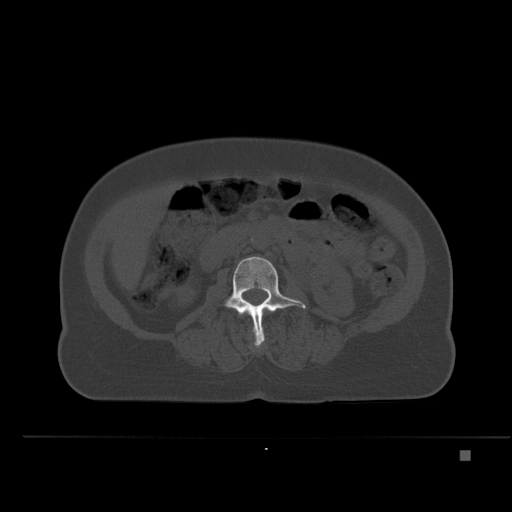
CT including the spine, one axial slice. Position 198 of 477 along the scan axis. Bone window (W 1800 / L 400 HU). 1.5 mm slice thickness. 512 × 512 image matrix, field of view 422 × 422 mm. Patient: female, 74 years. Case-level facts recorded for this patient, not image findings: primary cancer: colon.
Annotated regions visible in this slice (semi-automatic segmentation, software-assisted and operator-edited):
- L2 vertebra: bounding box (x1, y1, x2, y2) in pixels: (255, 331, 264, 343)
- L3 vertebra: (224, 256, 306, 346)